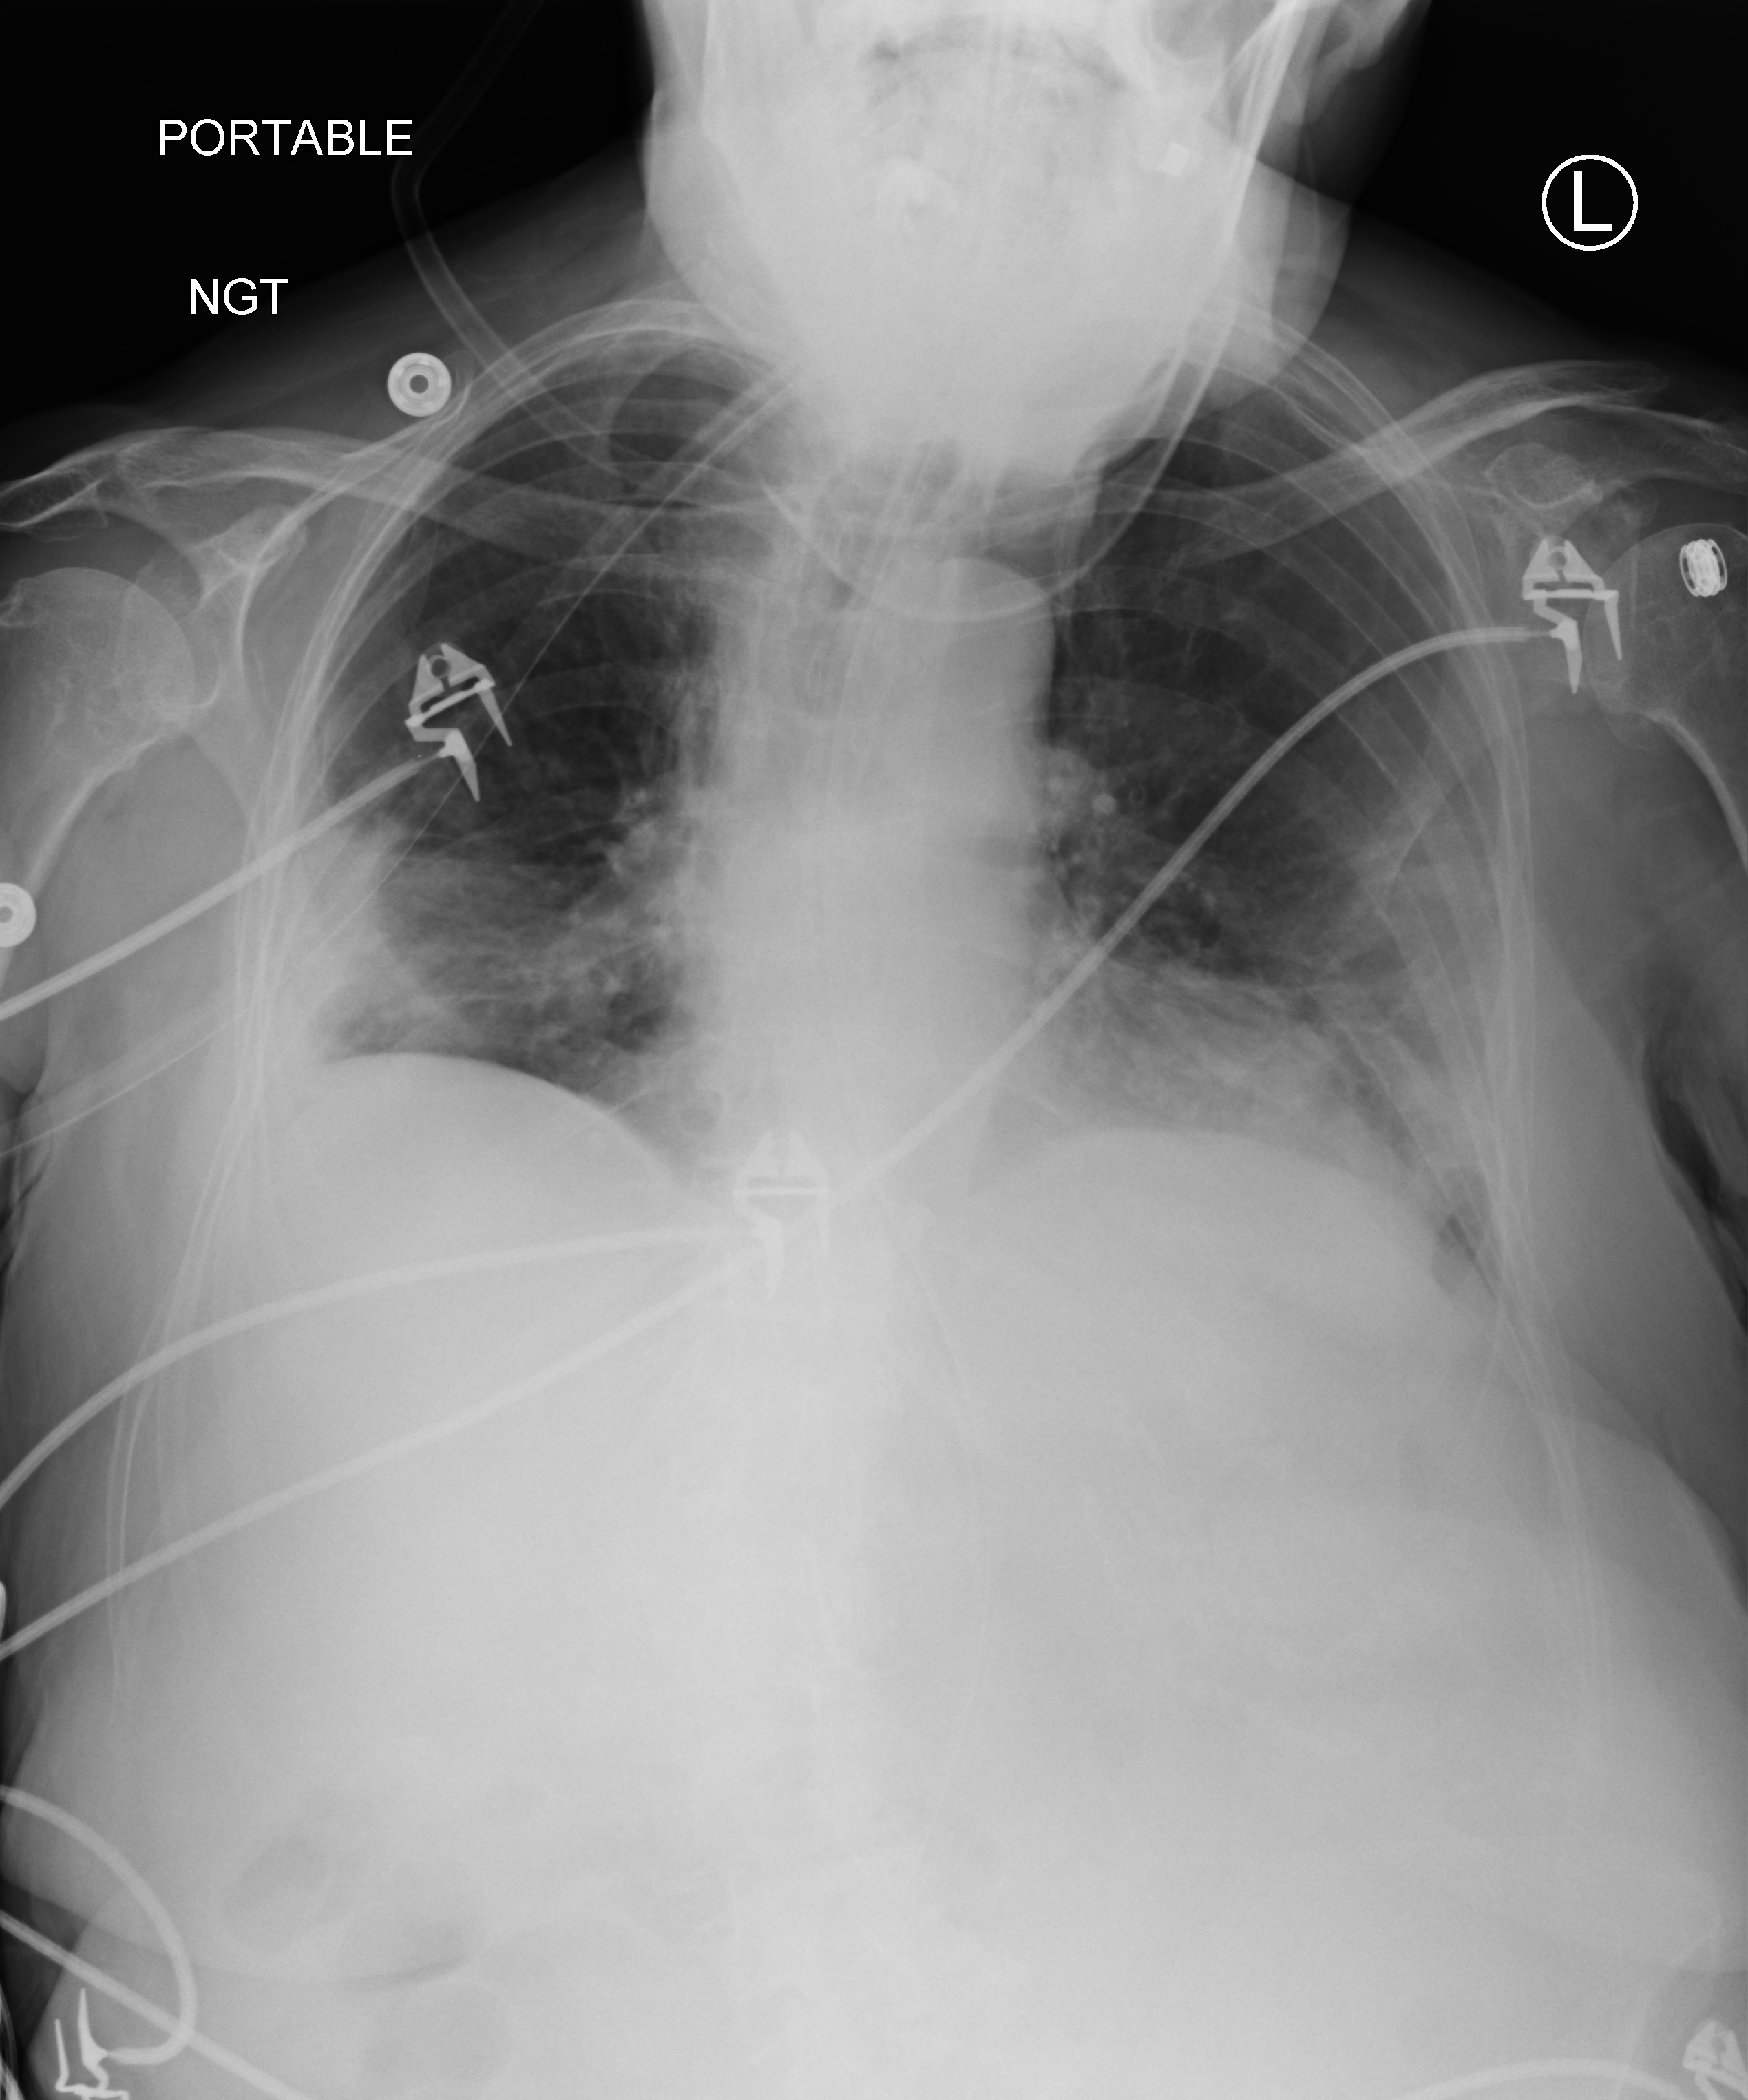
Portable chest radiograph; anteroposterior (AP) projection. Female patient hospitalised with COVID-19, age 75–90 years.
Hospital-stay facts (about this admission, not read from this image; timing relative to this image not recorded): mechanically ventilated during this hospital stay: yes; COPD (admission record): no; length of hospital stay: 82 days.